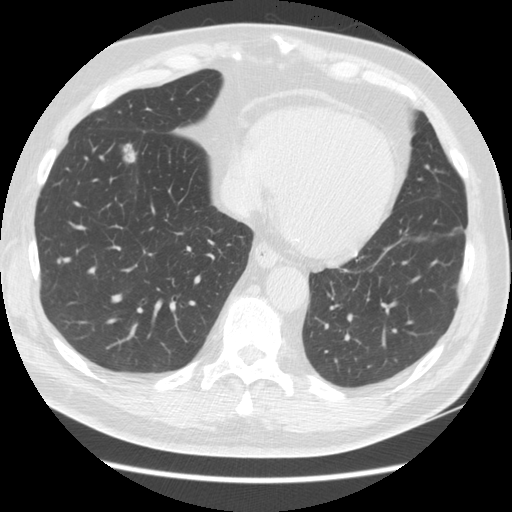
Low-dose screening chest CT, one axial slice. Position 50 of 161 along the scan axis. Reconstruction kernel STANDARD. 140 kVp. Lung window (W 1500 / L -600 HU). 2.5 mm slice thickness. 512 × 512 image matrix.
Structures marked on this image (manually delineated by an expert):
- lesion 1 (tumor, lower lobe of right lung): bounding box [x1, y1, x2, y2] px = [123, 143, 137, 163]